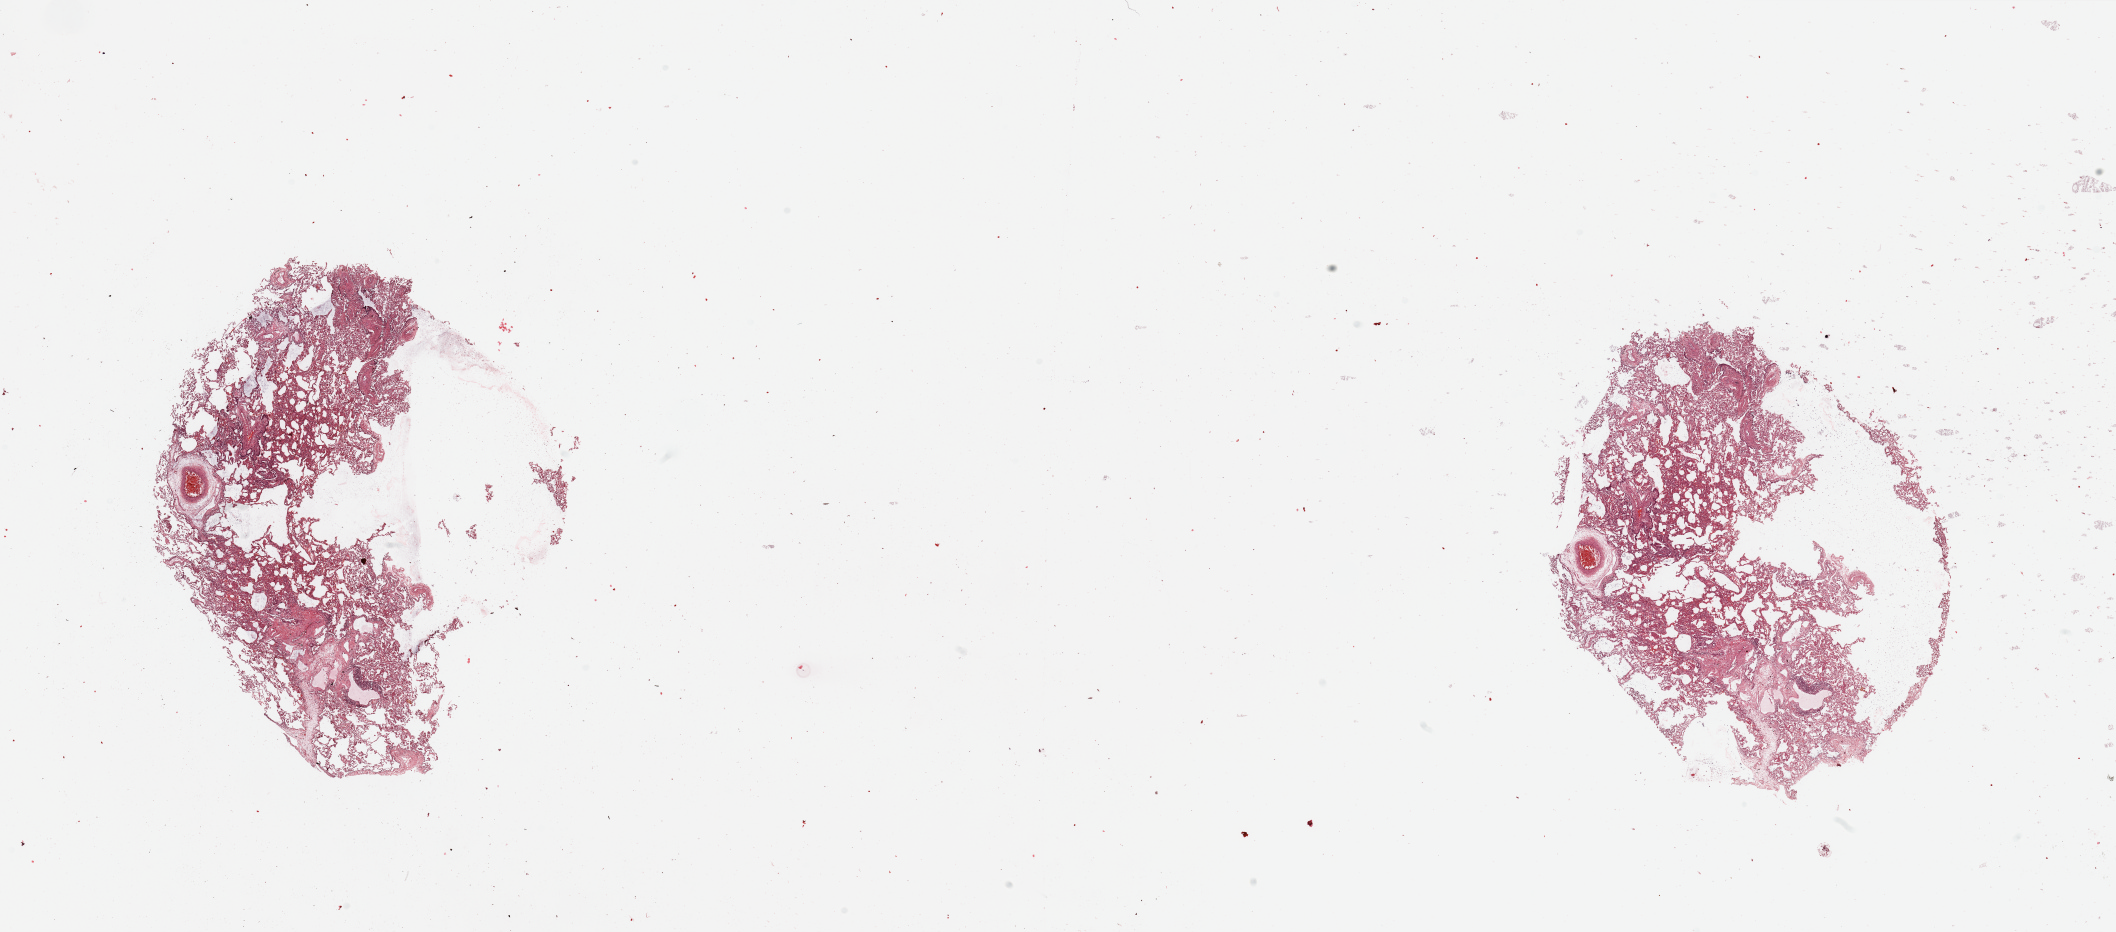
H&E-stained whole-slide image — shown as a low-resolution overview of the whole scanned area (about 33.5 x 14.7 mm, slide scanned at 20x); normal (non-tumour) tissue sample, sampled site: lung. Patient: male, age 59 years.
This section: normal (non-tumour) tissue from the same patient. Patient diagnosis: Adenocarcinoma, NOS.